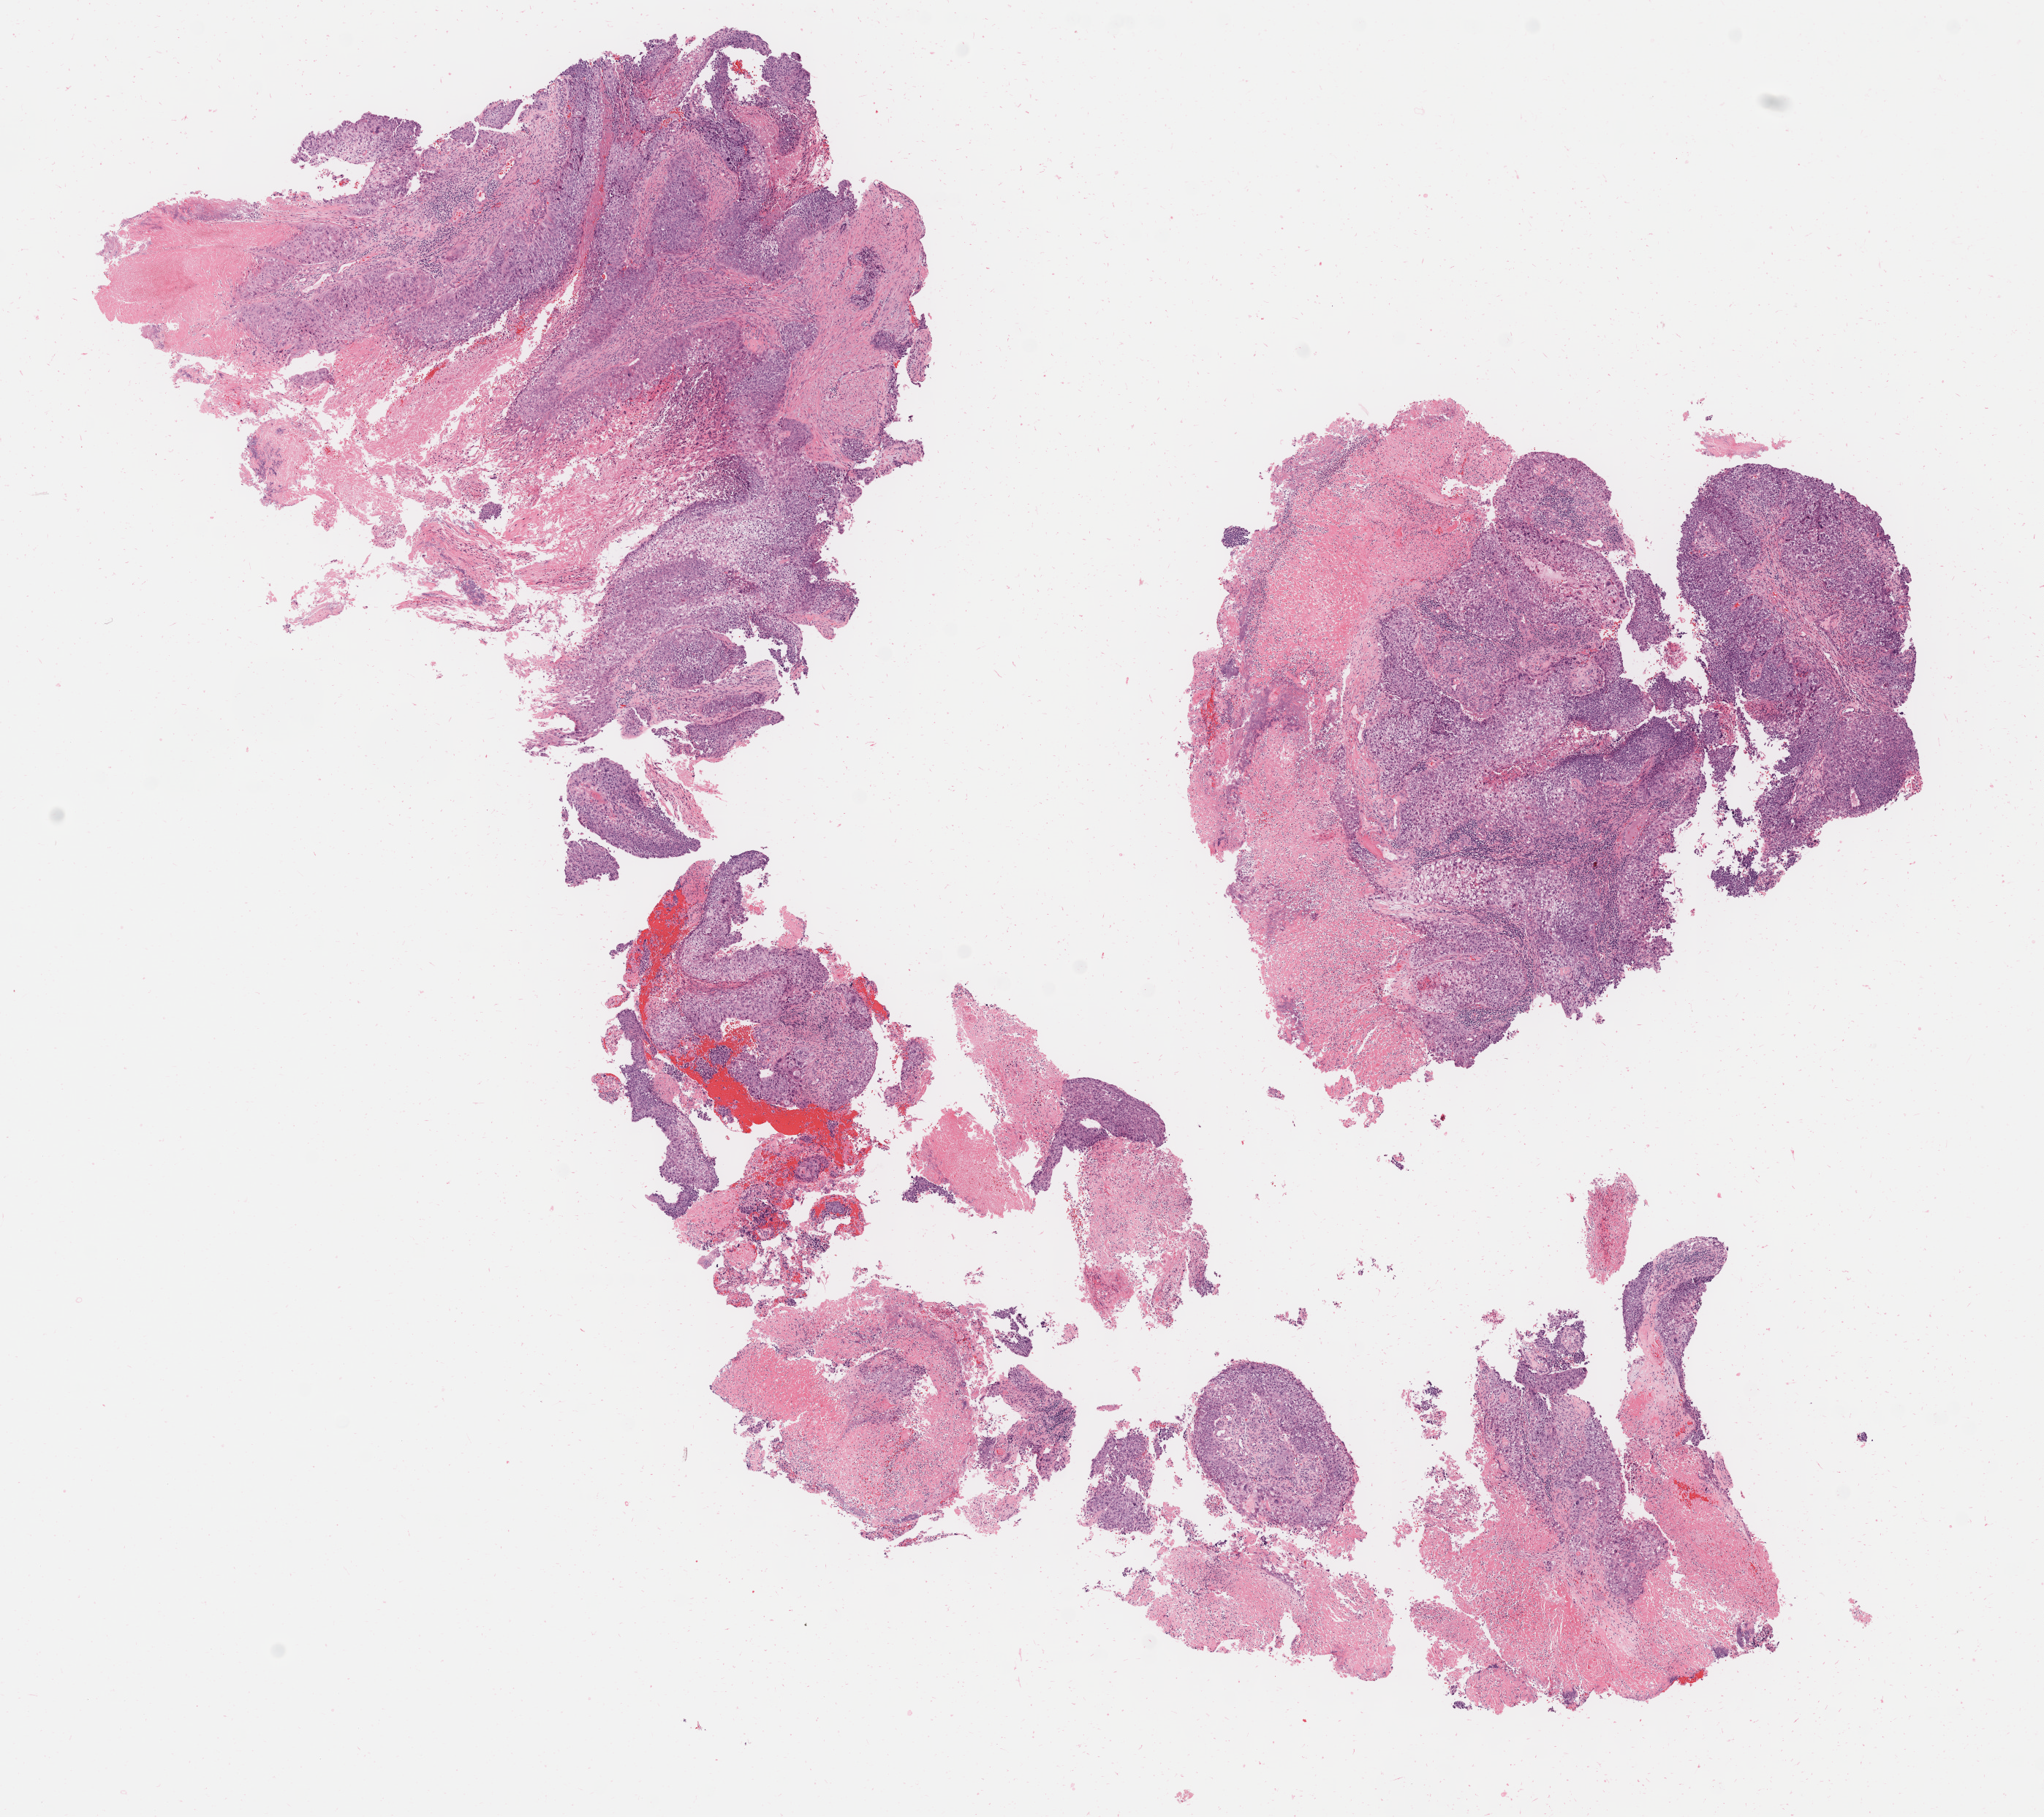
Whole-slide image, hematoxylin and eosin (H&E) stain — low-resolution overview of the scanned area, about 11.1 x 9.9 mm, specimen: tumor tissue, anatomic site: cervix. Patient female; 41 years old.
Histologic diagnosis: Squamous cell carcinoma, large cell, nonkeratinizing, NOS.